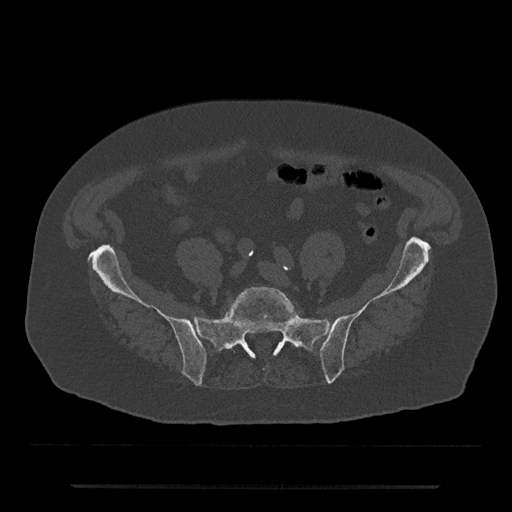
CT including the spine, one axial slice. Position 252 of 797 along the scan axis. Reconstruction kernel Br40s/3. Bone window (W 1800 / L 400 HU). 0.5 mm slice thickness. 512 × 512 image matrix, field of view 434 × 434 mm. Patient: male, 80 years. From the clinical record (not read from this slice): primary cancer: prostate; vertebrae with lytic lesions (as recorded): L1, T11.
Annotated regions visible in this slice (semi-automatically segmented with operator editing):
- L5 vertebra: bounding box [x1, y1, x2, y2] px = [226, 287, 298, 350]